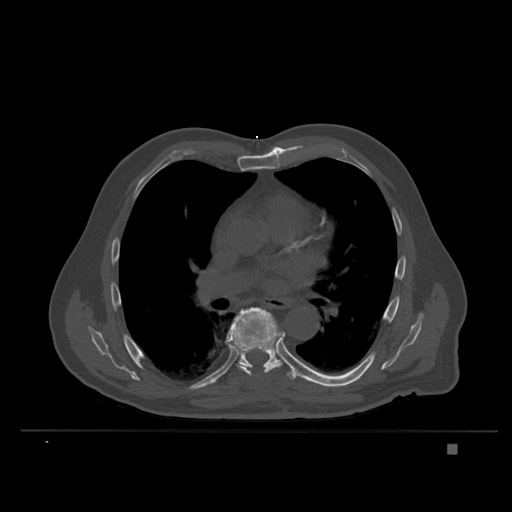
CT including the spine, one axial slice. Position 238 of 435 along the scan axis. Bone window (W 1800 / L 400 HU). 1.5 mm slice thickness. 512 × 512 image matrix, field of view 434 × 434 mm. Patient: male, 73 years. From the clinical record (not read from this slice): primary cancer: skin.
Outlined on this slice (semi-automatic segmentation, software-assisted and operator-edited):
- T7 vertebra: bounding box <226,307,283,376> (left, top, right, bottom; pixels)
- T8 vertebra: <239,322,301,380>